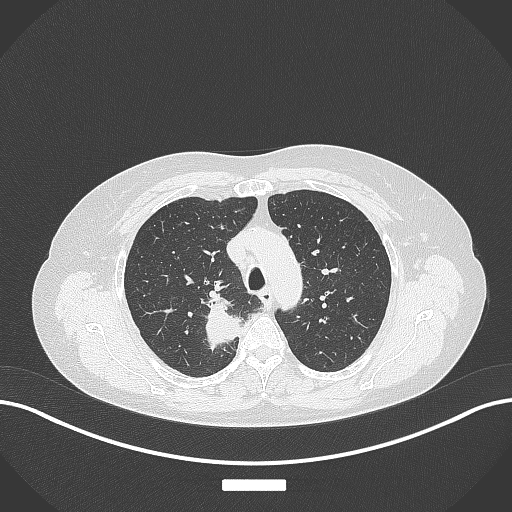
Chest CT, one axial slice. Position 288 of 357 along the scan axis. Reconstruction kernel B70f. Lung window (W 1500 / L -600 HU). 512 × 512 image matrix, field of view 400 × 400 mm. Female patient, age 62 years. From the clinical record (not read from this slice): clinical TNM (as recorded): T1c N1 M0.
Structures marked on this image (rectangle marked by the reading radiologist):
- lung tumour (recorded histology: squamous cell carcinoma): bounding box <202,295,244,350> (left, top, right, bottom; pixels)